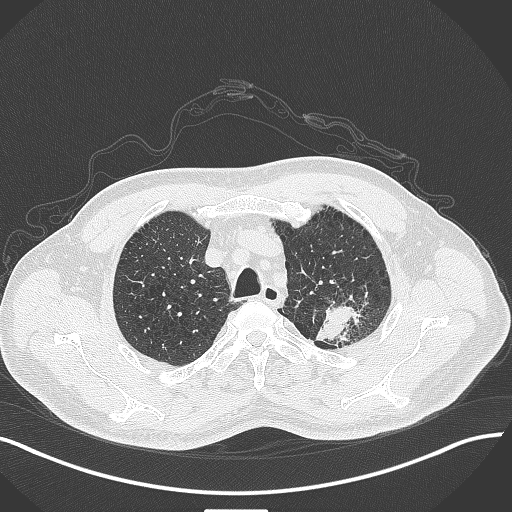
Chest CT, one axial slice; position 348 of 429 along the scan axis; reconstruction kernel B70f; lung window (W 1500 / L -600 HU); 512 × 512 image matrix, field of view 400 × 400 mm. Male patient, age 55 years. Case-level facts recorded for this patient, not image findings: clinical TNM (as recorded): T3 N0 M1c.
Structures marked on this image (bounding box drawn by a radiologist):
- lung tumour (recorded histology: adenocarcinoma): box from (x=316, y=297) to (x=373, y=350) px